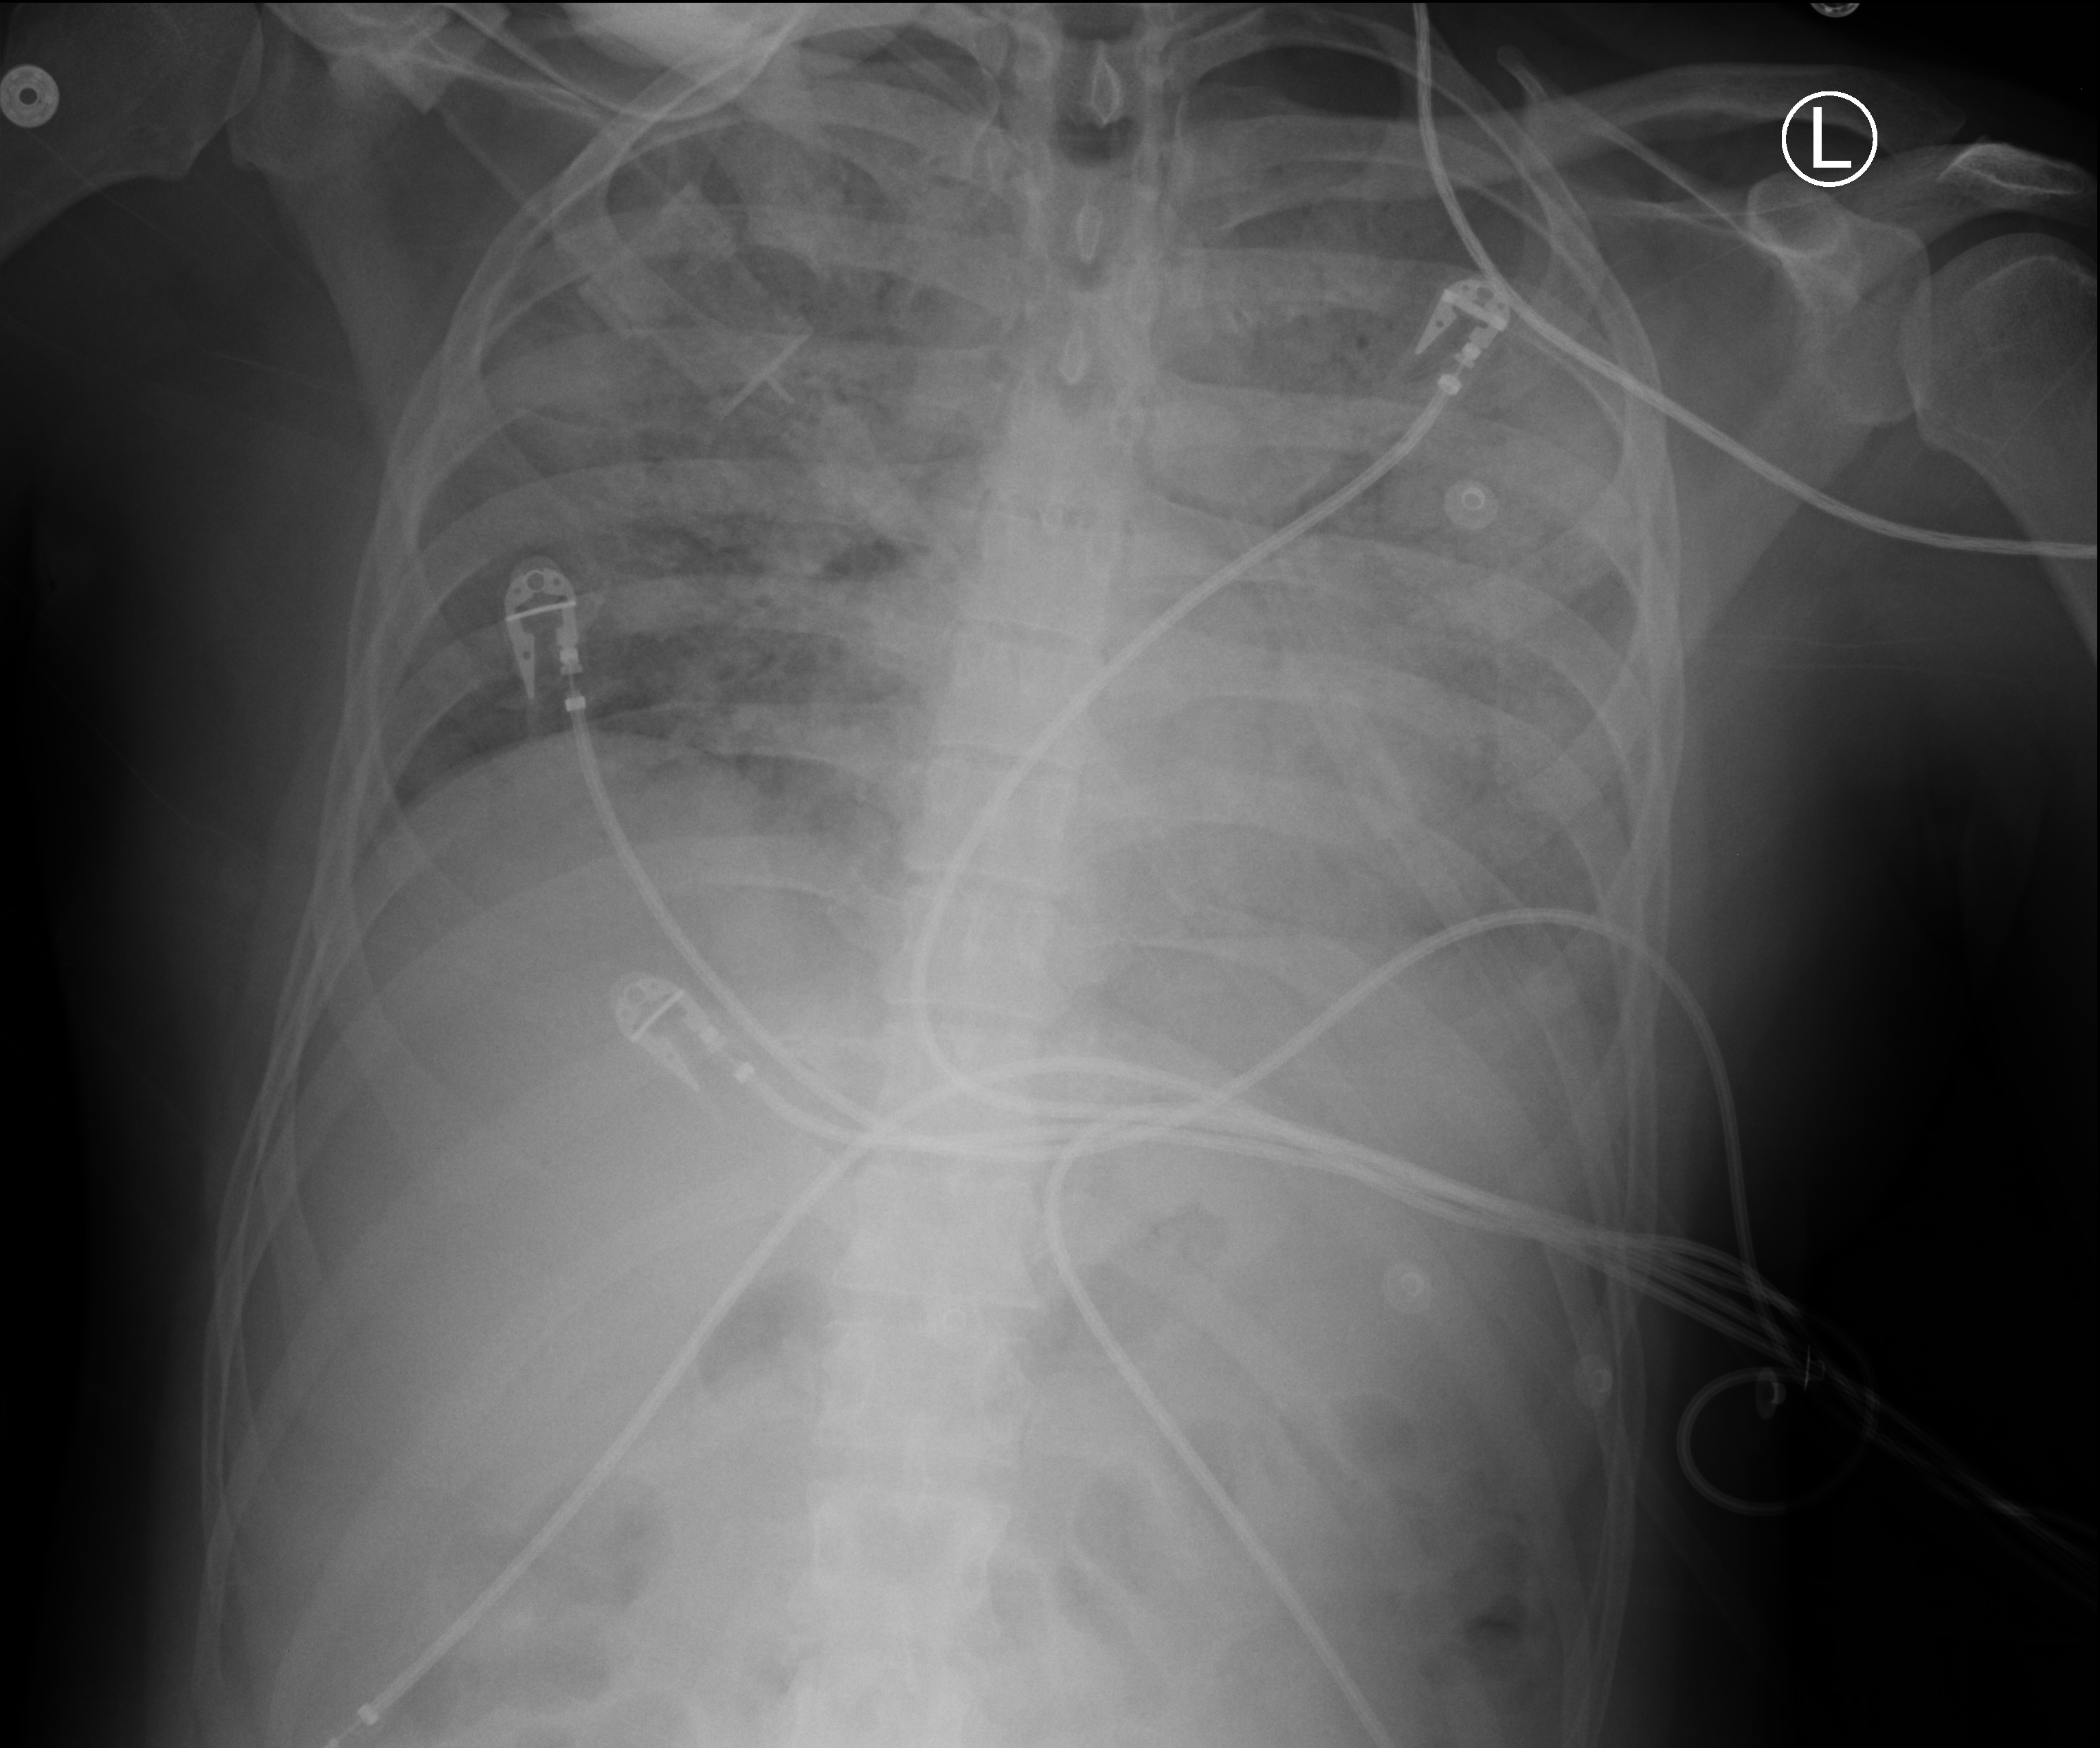
Portable chest radiograph; anteroposterior (AP) projection. Male patient hospitalised with COVID-19, age 18–59 years.
From the hospital-stay record, not from the radiograph (when in the stay this image was taken is not recorded): mechanically ventilated during this hospital stay: yes.